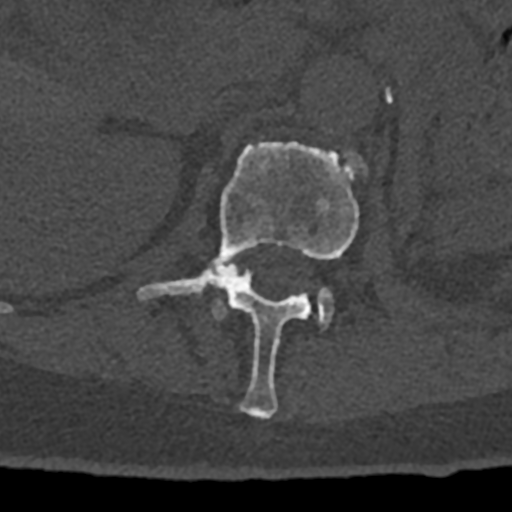
CT including the spine, one axial slice. Position 425 of 797 along the scan axis. Bone window (W 1800 / L 400 HU). 0.5 mm slice thickness. 512 × 512 image matrix. Patient: male, 74 years. Case-level facts recorded for this patient, not image findings: primary cancer: renal.
Structures marked on this image (semi-automatically segmented with operator editing):
- L1 vertebra: bounding box [x1, y1, x2, y2] px = [137, 141, 365, 418]
- L2 vertebra: [213, 292, 333, 326]